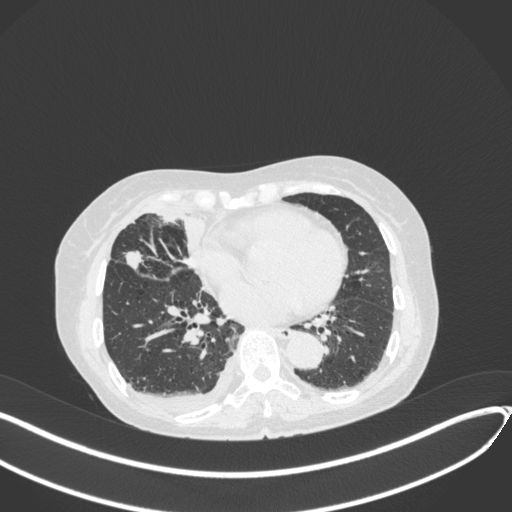
Chest CT, one axial slice. Position 160 of 418 along the scan axis. Reconstruction kernel B31f. 120 kVp. Lung window (W 1500 / L -600 HU). 1 mm slice thickness. 512 × 512 image matrix, field of view 400 × 400 mm. Patient: female, 75 years. Case-level facts recorded for this patient, not image findings: clinical TNM (as recorded): T2a N3 M0.
Outlined on this slice (bounding box drawn by a radiologist):
- lung tumour (recorded histology: adenocarcinoma): bounding box <122,249,144,271> (left, top, right, bottom; pixels)